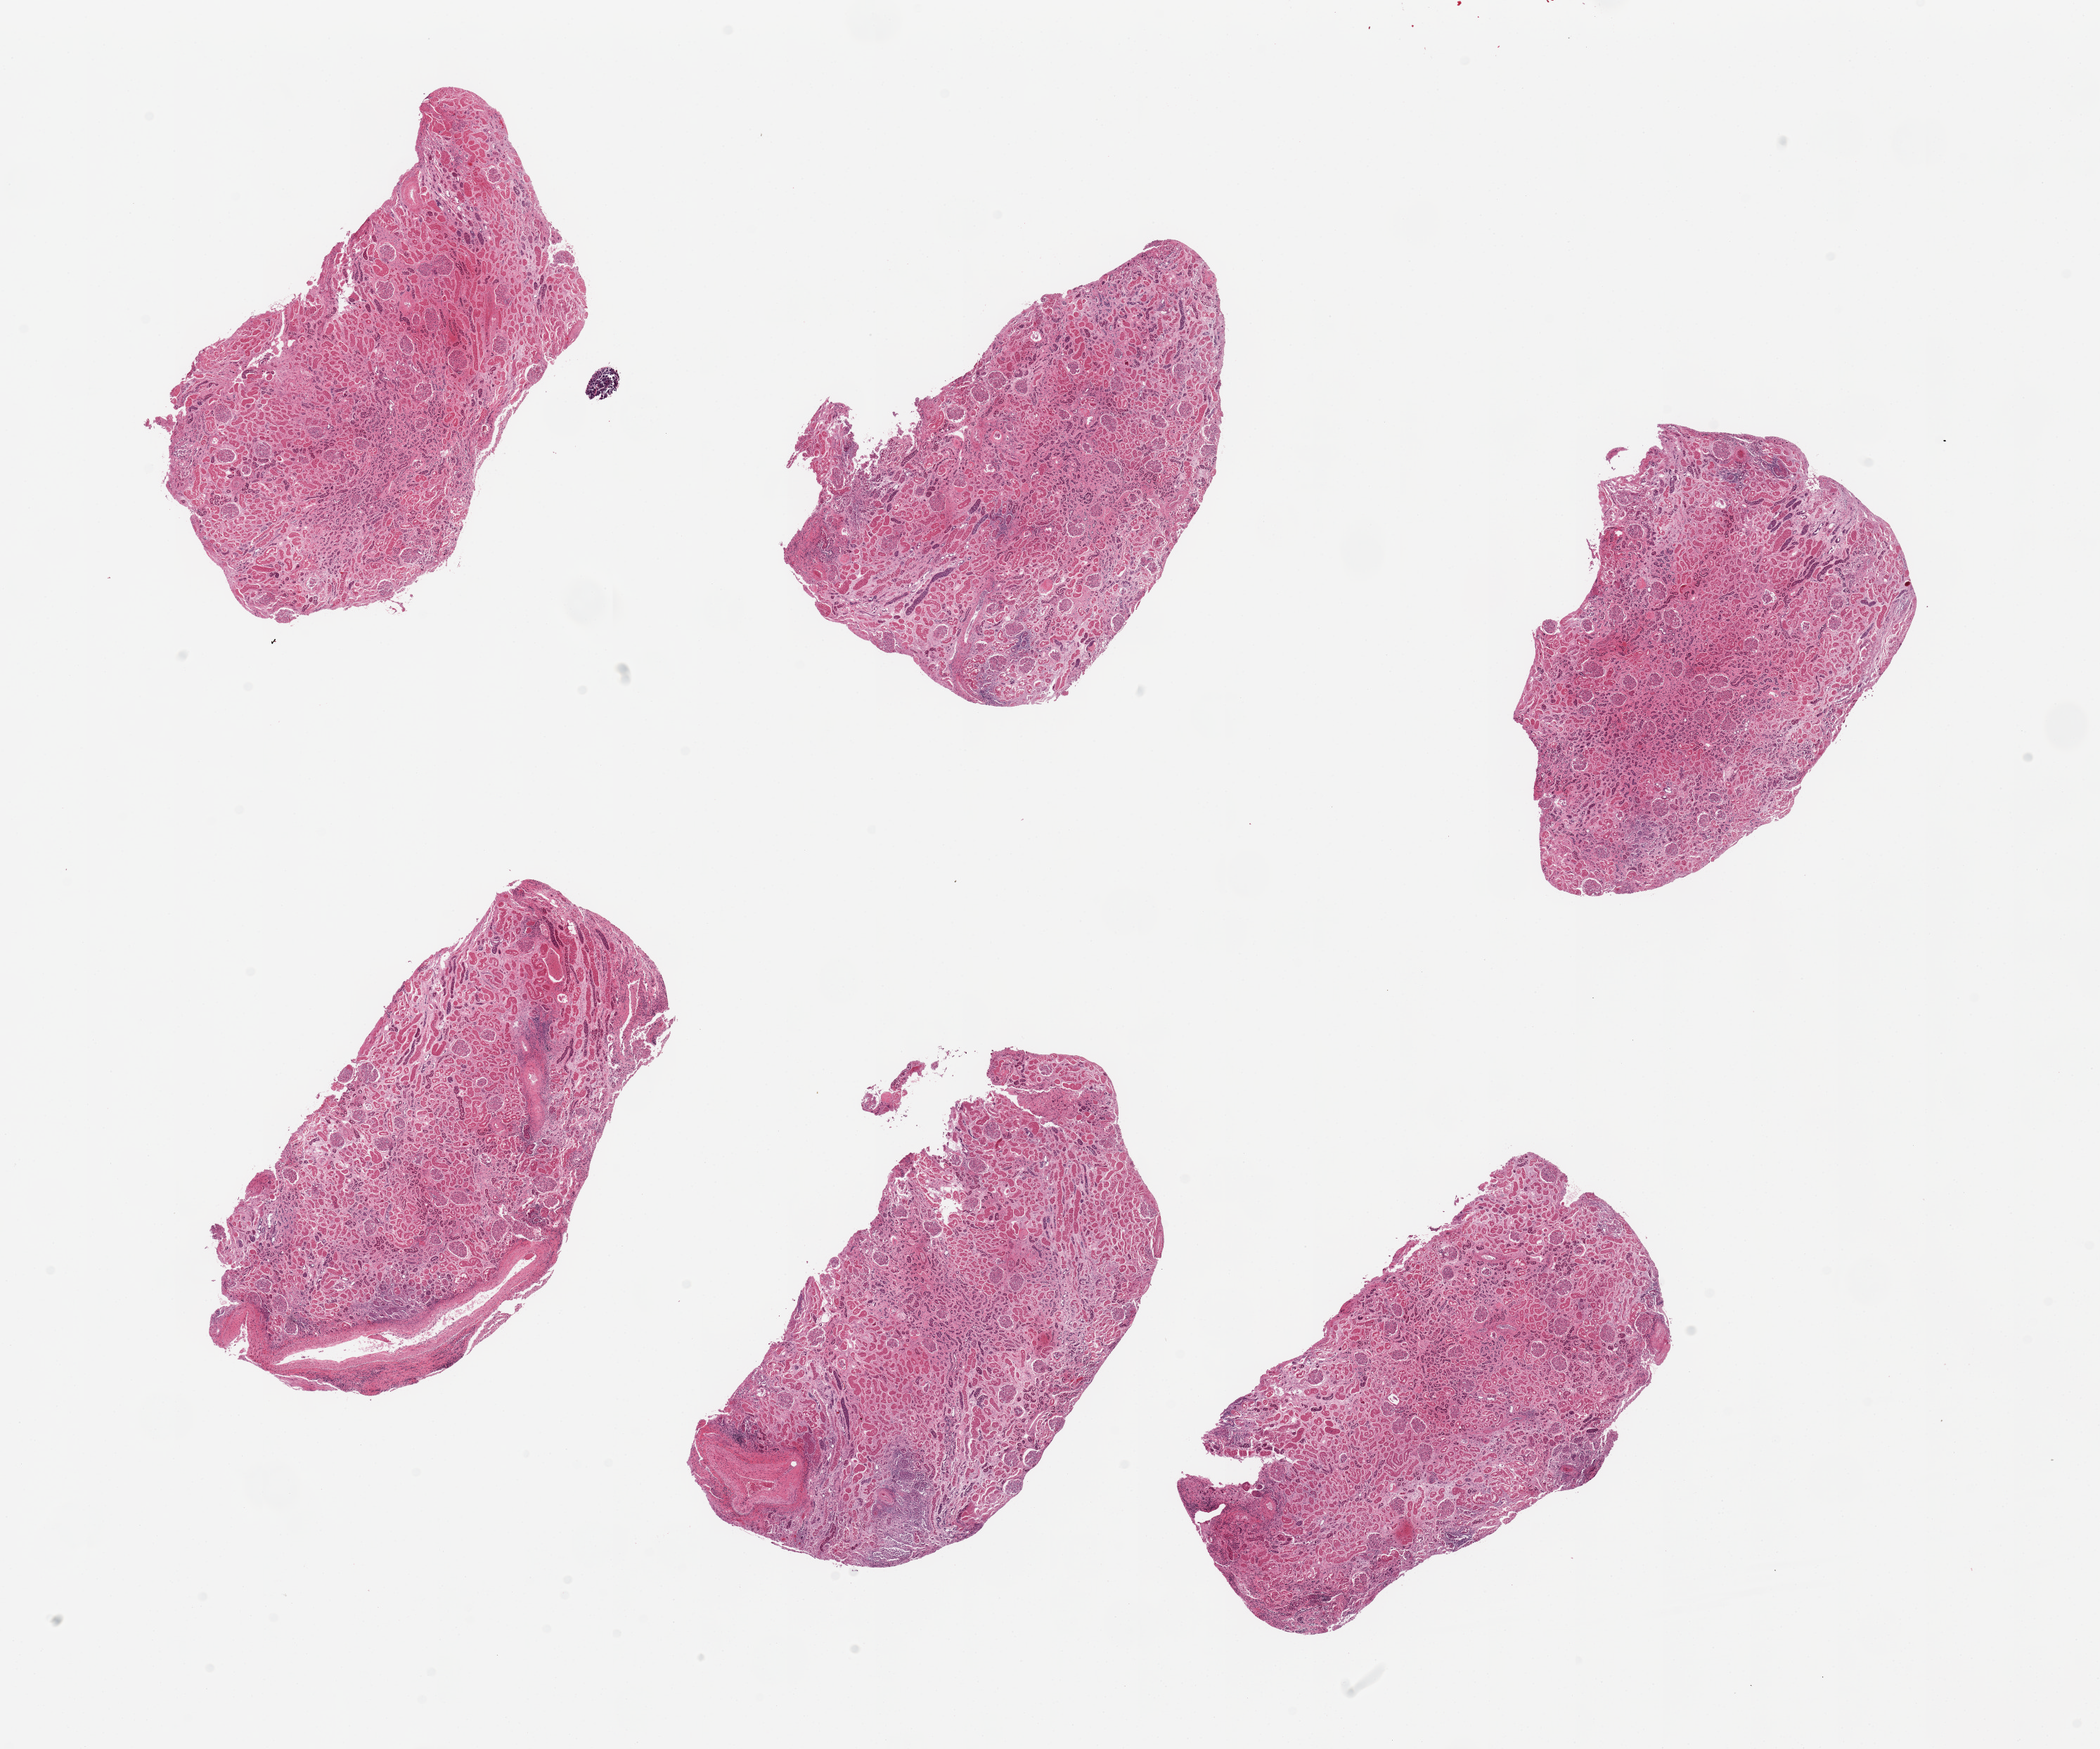
Haematoxylin and eosin whole-slide image — a low-resolution overview of the entire scanned area, about 23.6 x 19.7 mm (slide scanned at 20x); PAXgene-fixed paraffin-embedded (PFPE) section; section of renal cortex (target tissue); tissue donor sample.
Pathologist's review note for this sample: 2 pieces, glomeruli present, all sections, tubules with moderate - marked autolysis.